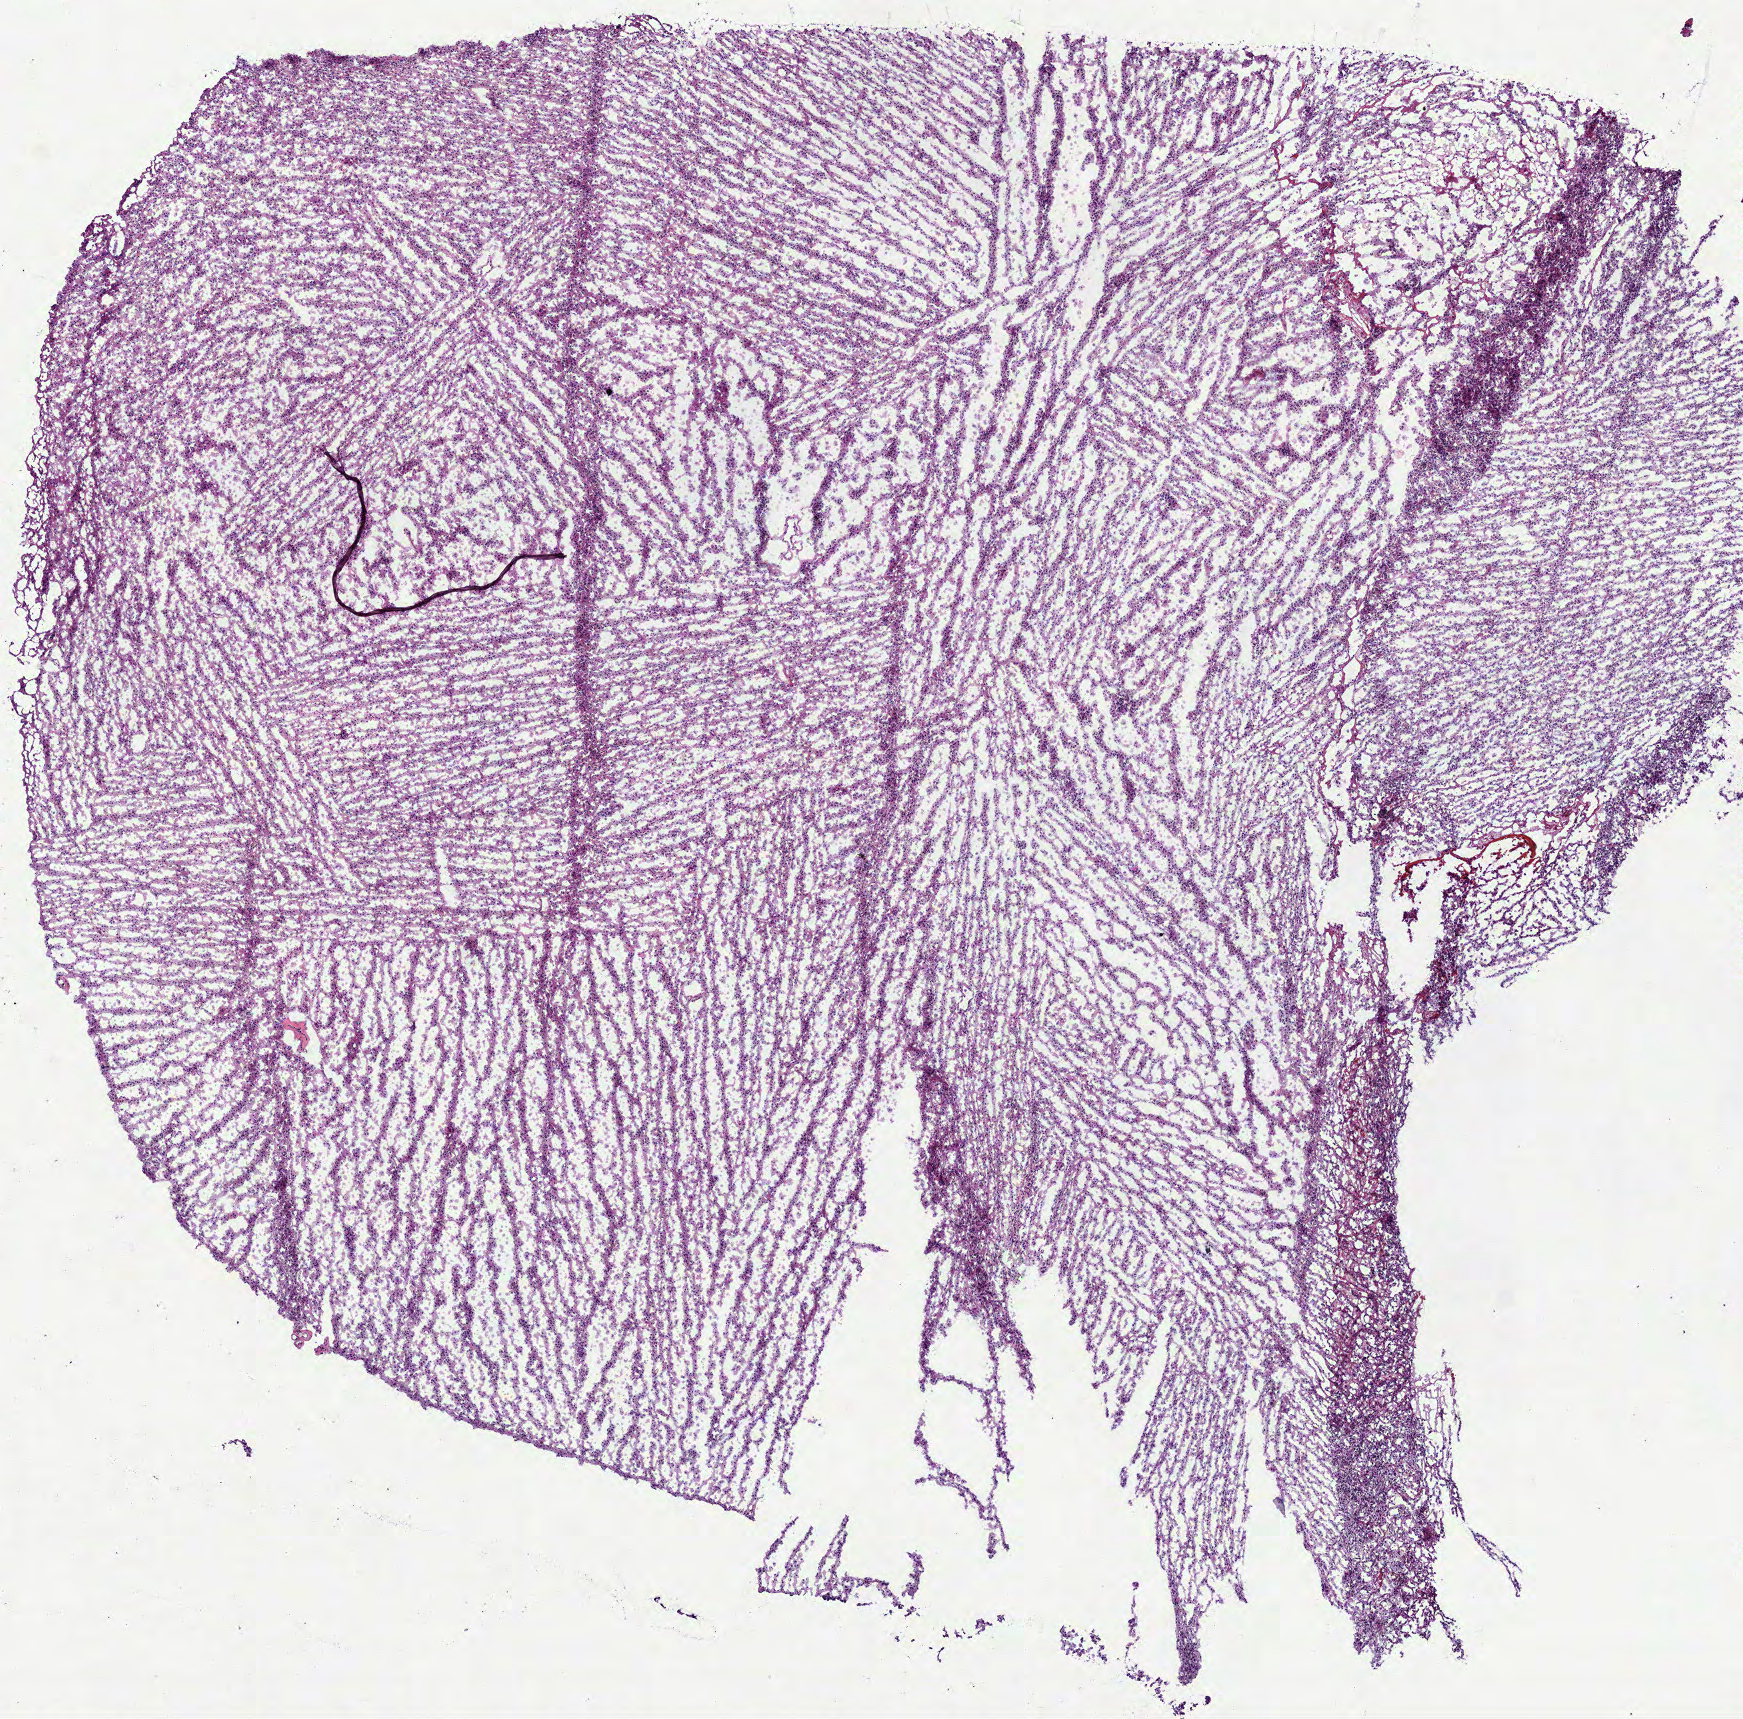
H&E-stained whole-slide image, a low-resolution overview of the entire scanned area, about 7.0 x 6.9 mm (from a 40x scan). Frozen section from the bottom of the tissue portion. Brain, primary tumour sample. Patient: female, age at initial diagnosis 57 years. Histologic grade: G2 (moderately differentiated). Composition of this section per pathologist review: tumour cells 100%, tumour nuclei 80%, normal cells 0%, stromal cells 0%, necrosis 0%.
Laterality: left. Pathologic diagnosis: Oligodendroglioma, NOS.